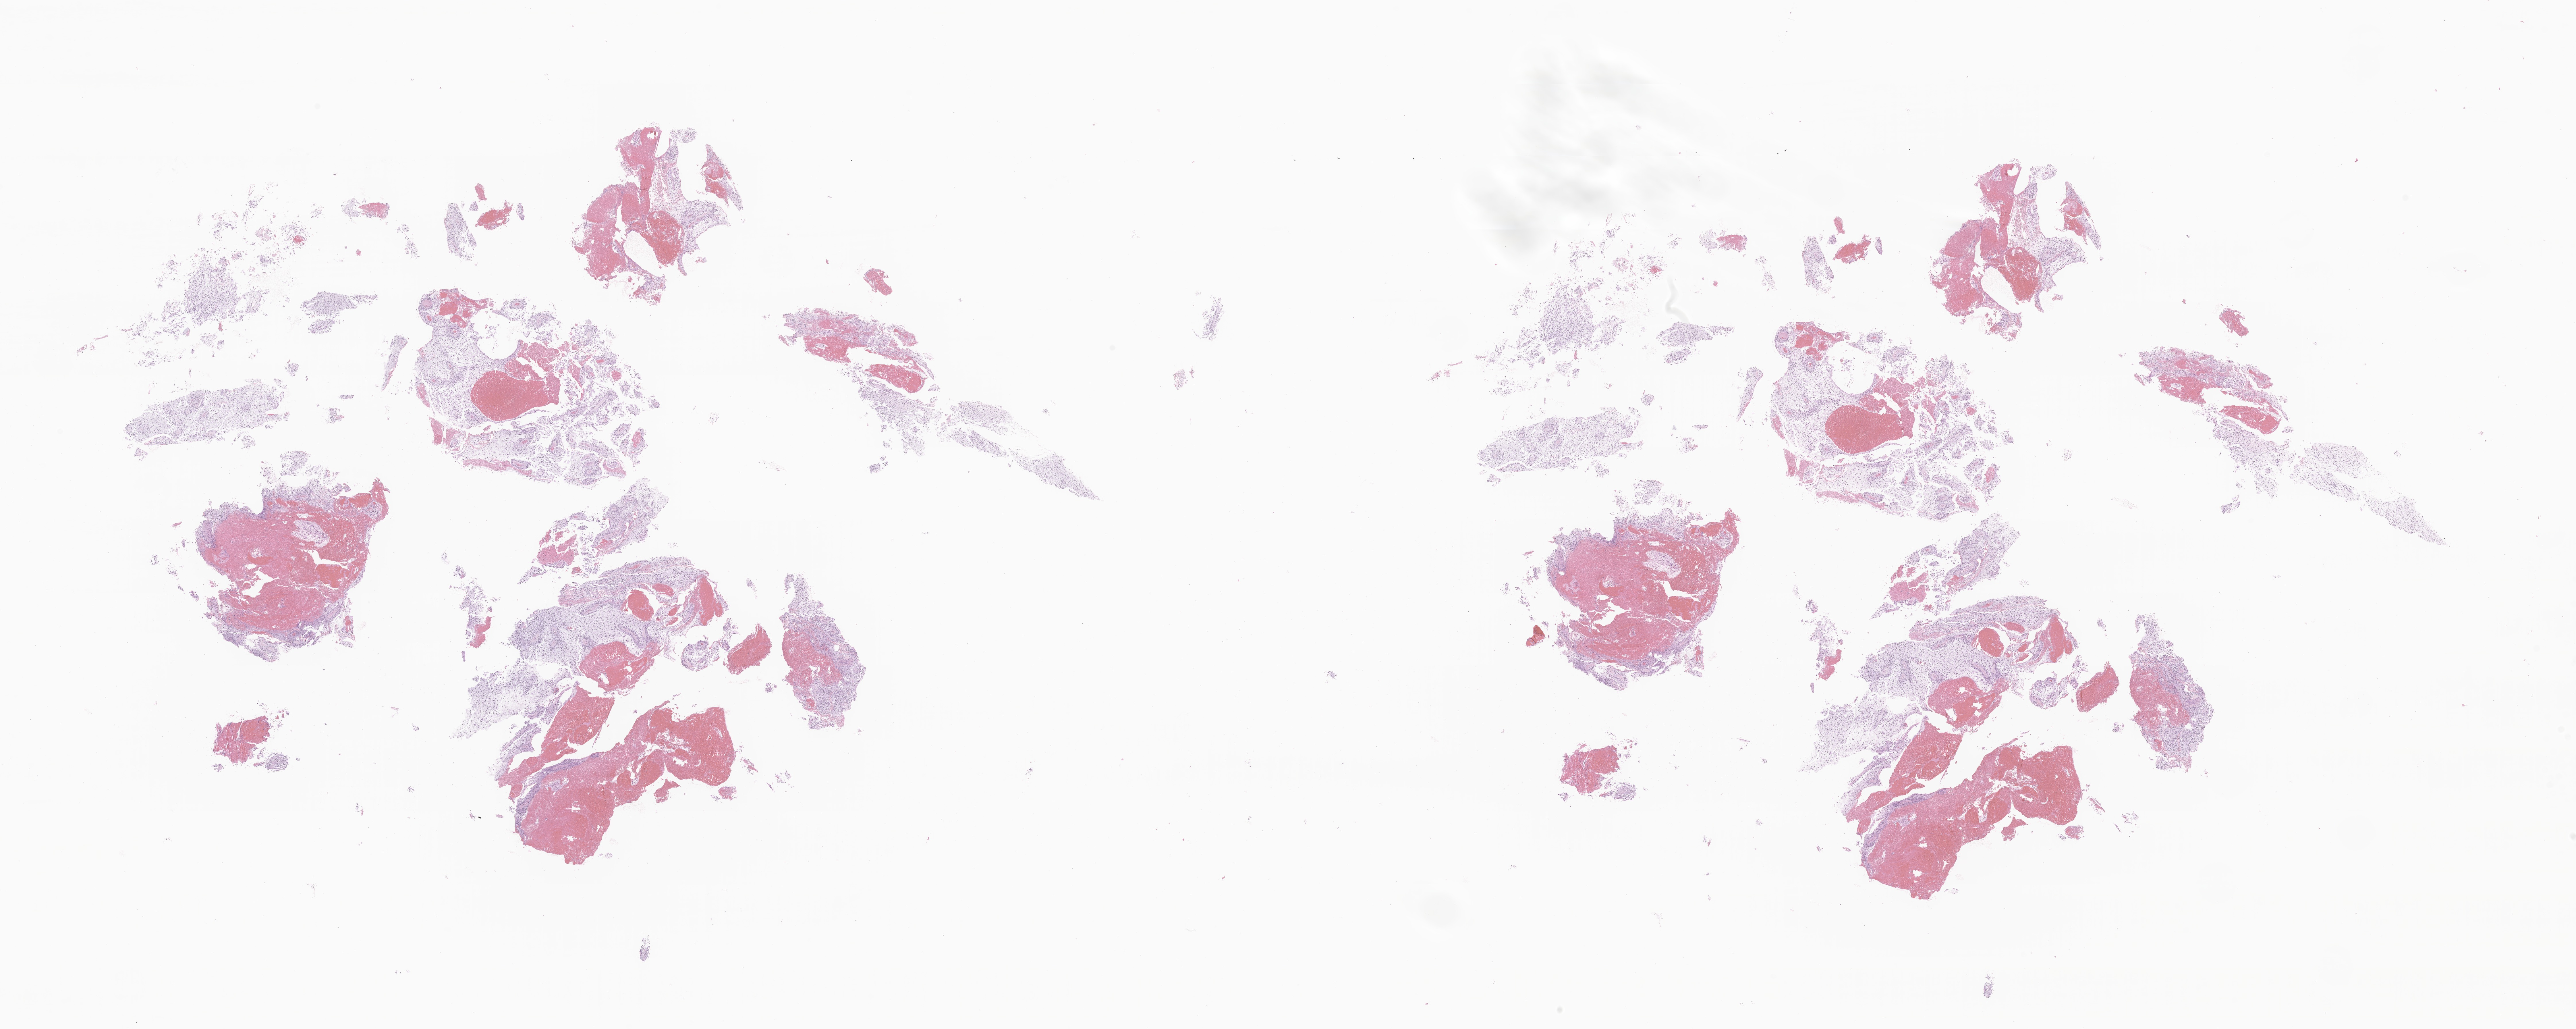
Digitized haematoxylin and eosin-stained section of tumor tissue from the brain, shown as a low-resolution overview of the whole scanned area (about 37.8 x 15.1 mm); FFPE section. Patient: male, age 166 days.
Diagnosis (ICD-O-3 morphology term): Neoplasm, uncertain whether benign or malignant.